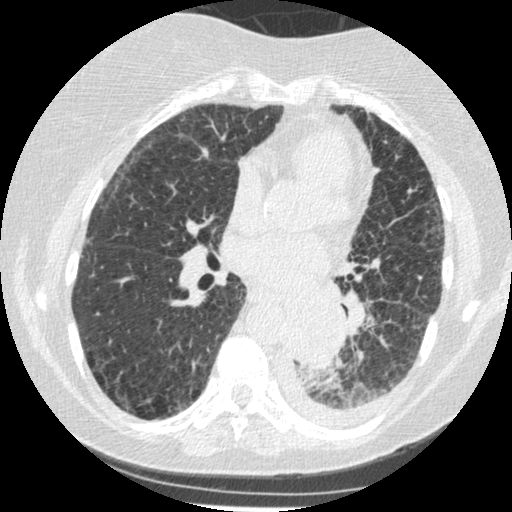
Low-dose screening chest CT, one axial slice. Slice 116 of 341 in the series (ordered by position). Reconstruction kernel STANDARD. 120 kVp. Lung window (W 1500 / L -600 HU). 1.25 mm slice thickness. 512 × 512 image matrix, field of view 310 × 310 mm.
Annotated regions visible in this slice (expert manual segmentation):
- lesion 1 (tumor, lower lobe of left lung): bounding box [x1, y1, x2, y2] px = [284, 301, 343, 366]